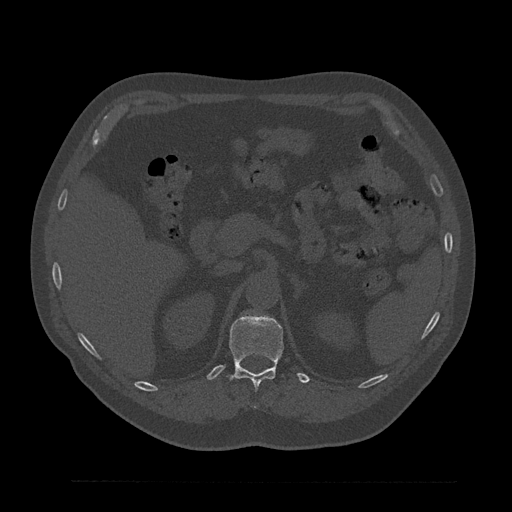
CT including the spine, one axial slice; slice 224 of 797 in the series (ordered by position); bone window (W 1800 / L 400 HU); 0.5 mm slice thickness; 512 × 512 image matrix, field of view 430 × 430 mm. Patient: male, 61 years. From the clinical record (not read from this slice): primary cancer: prostate.
Structures marked on this image (semi-automatic segmentation, software-assisted and operator-edited):
- T12 vertebra: bounding box (x1, y1, x2, y2) in pixels: (229, 314, 283, 390)